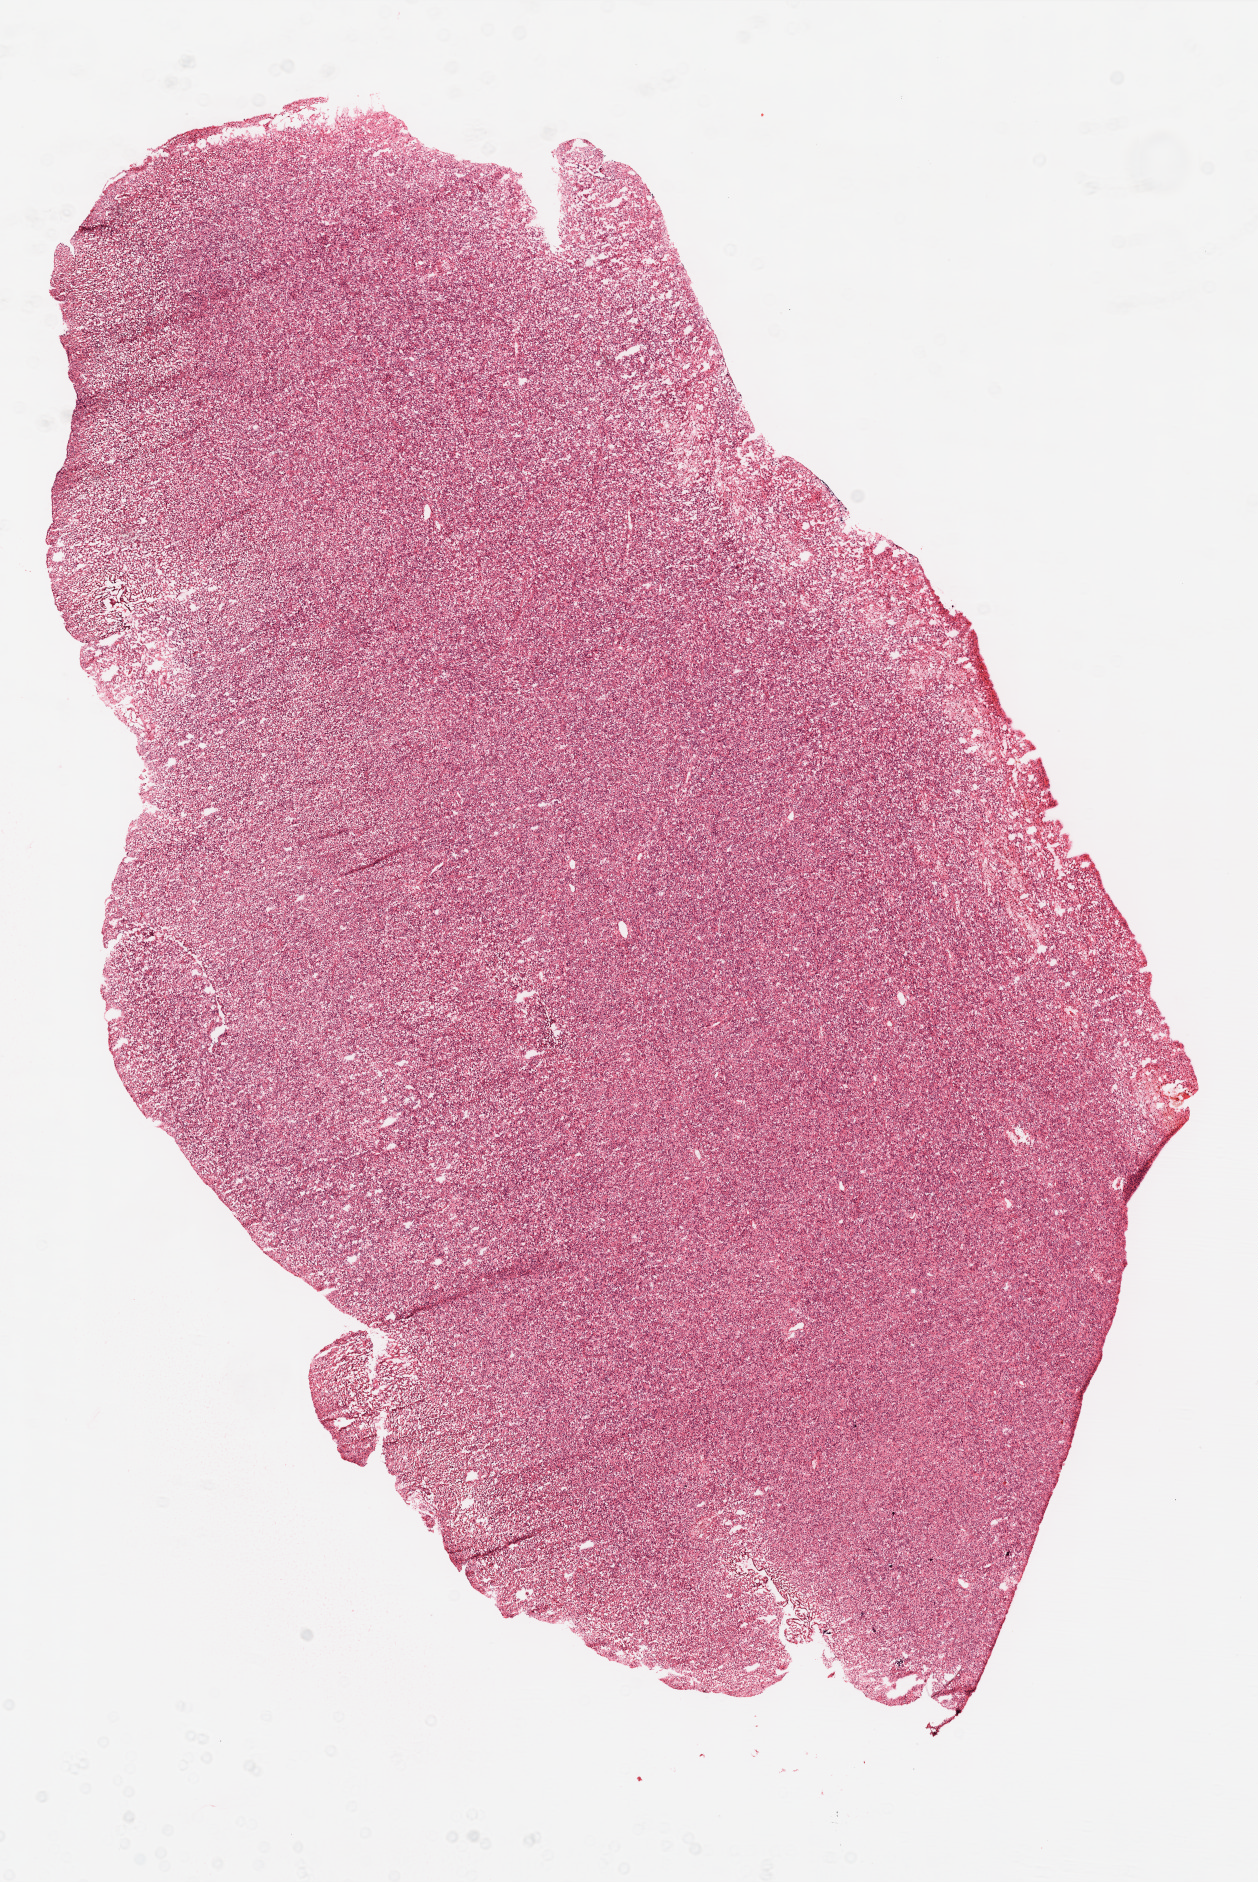
Digitized H&E-stained tissue section (whole slide), low-resolution overview of the scanned area, about 10.1 x 15.1 mm (slide scanned at 20x), frozen section from the top of the tissue portion, sample: primary tumour, brain. Female, age 61 years at initial diagnosis. Slide review estimates, as recorded: tumour cells 100%, tumour nuclei 100%, normal cells 0%, stromal cells 0%, necrosis 5%.
• pathologic diagnosis: Glioblastoma